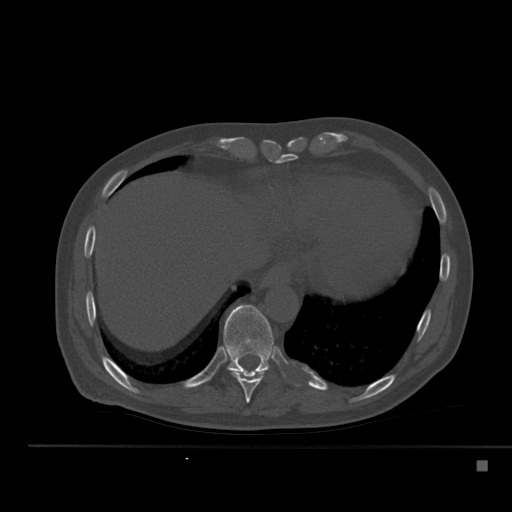
CT including the spine, one axial slice. Position 278 of 517 along the scan axis. Reconstruction kernel Br40s. 120 kVp. Bone window (W 1800 / L 400 HU). 1.5 mm slice thickness. 512 × 512 image matrix. Male patient, age 70 years. From the clinical record (not read from this slice): primary cancer: renal; vertebrae with lytic lesions (as recorded): T4, T6, T10, T12, L3, L4, L5.
Annotated regions visible in this slice (semi-automatically segmented with operator editing):
- T10 vertebra: bounding box <223,305,277,376> (left, top, right, bottom; pixels)
- T9 vertebra: <230,370,266,403>